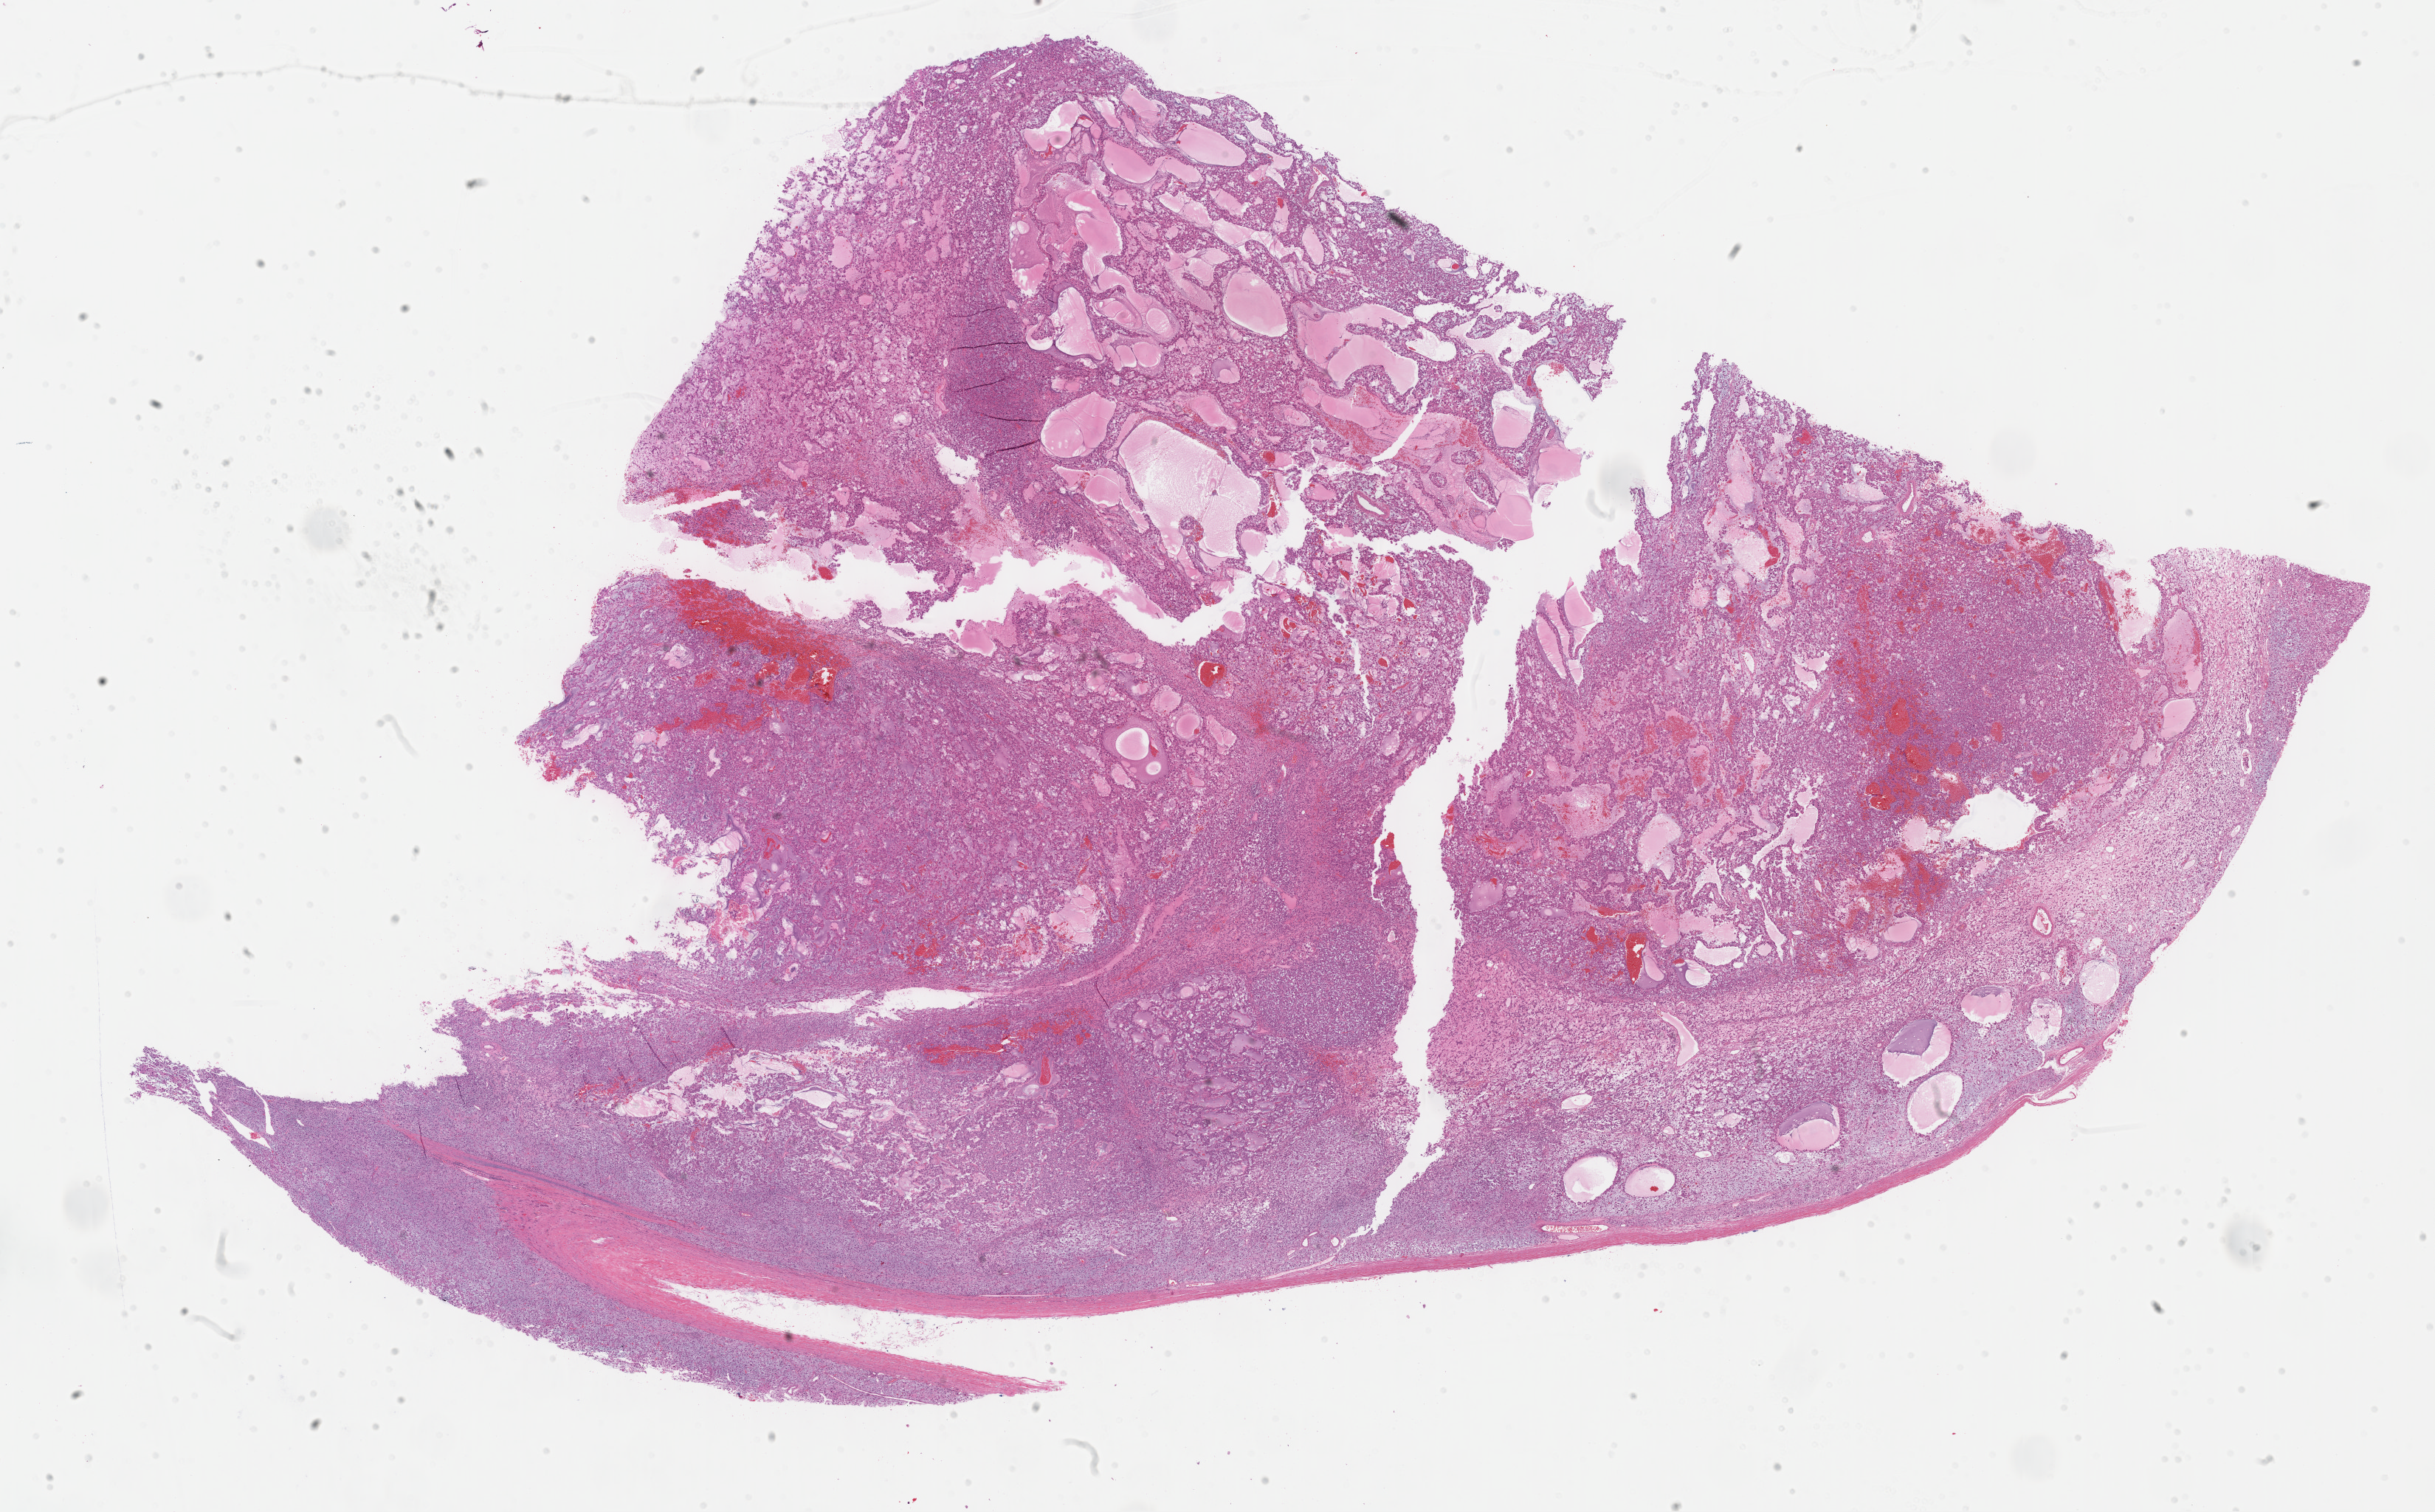
Digitized Hematoxylin and eosin (H&E) stained tissue section (whole slide), shown as a low-resolution overview of the whole scanned area (about 26.7 x 16.6 mm, acquisition: 40x scan). FFPE section. Sample: primary tumour, adrenal cortex. Female patient; age at initial diagnosis 26 years.
Pathologic diagnosis: Adrenal cortical carcinoma (cortex of adrenal gland).